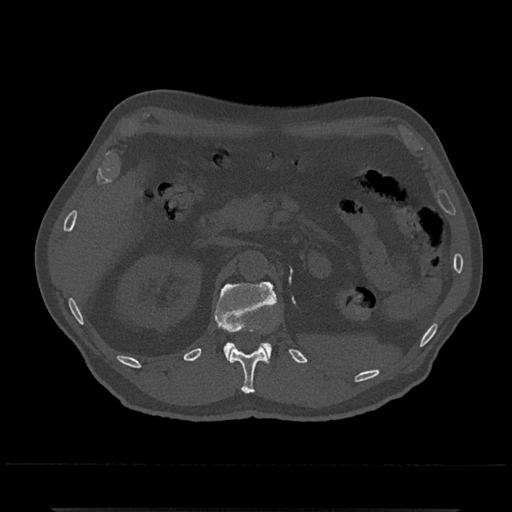
CT including the spine, one axial slice; position 399 of 797 along the scan axis; bone window (W 1800 / L 400 HU); 512 × 512 image matrix, field of view 393 × 393 mm. Male patient, age 67 years. From the clinical record (not read from this slice): primary cancer: prostate.
Outlined on this slice (semi-automatic segmentation, software-assisted and operator-edited):
- L1 vertebra: bounding box [x1, y1, x2, y2] px = [215, 282, 277, 363]
- T12 vertebra: [230, 330, 268, 394]